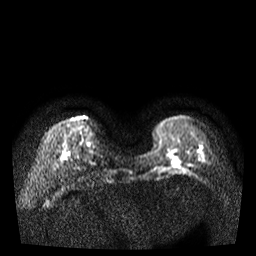
Breast MRI, one axial slice. Position 10 of 35 along the scan axis. Diffusion-weighted series; image 2 of 4 stored at this slice position (different b-values; order by instance number). 3 T. 5 mm slice thickness. 256 × 256 image matrix, field of view 320 × 320 mm. Female patient.
Outlined on this slice (expert manual segmentation):
- tumour on diffusion-weighted imaging: bounding box (x1, y1, x2, y2) in pixels: (174, 160, 180, 164)